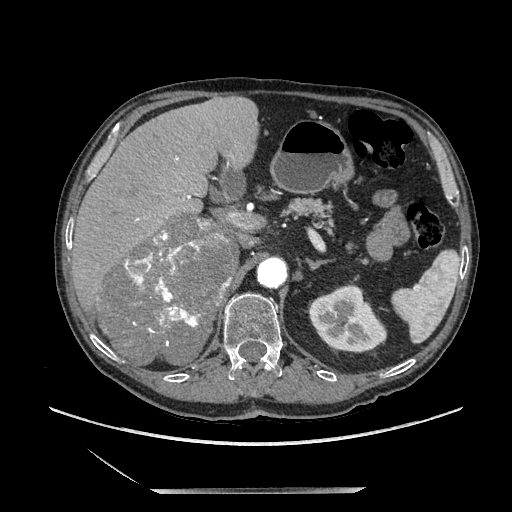
Contrast-enhanced abdominal CT, one axial slice; slice 131 of 243 in the series (ordered by position); soft-tissue window (W 400 / L 40 HU); 1.25 mm slice thickness; 512 × 512 image matrix. Male patient. Case-level facts recorded for this patient, not image findings: diagnosis: adrenocortical carcinoma; tumour side: right adrenal.
Annotated regions visible in this slice (semi-automatically segmented with operator editing):
- mass: box from (x=101, y=215) to (x=238, y=366) px